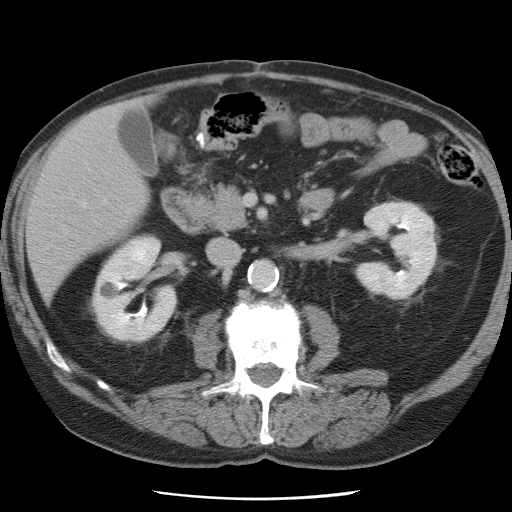
Contrast-enhanced abdominal CT, one axial slice; slice 29 of 78 in the series (ordered by position); 120 kVp; intravenous contrast given; soft-tissue window (W 400 / L 40 HU); 5 mm slice thickness; 512 × 512 image matrix, field of view 337 × 337 mm. Male patient, age 75 years. From the clinical record (not read from this slice): diagnosis: colorectal cancer liver metastases, imaged before liver resection; multiple liver metastases: yes; largest metastasis: 2.4 cm; chemotherapy before resection: yes.
Structures marked on this image (manually delineated by an expert):
- liver: bounding box <29,104,148,297> (left, top, right, bottom; pixels)
- planned liver remnant (the part of the liver to remain after resection): <29,117,149,297>